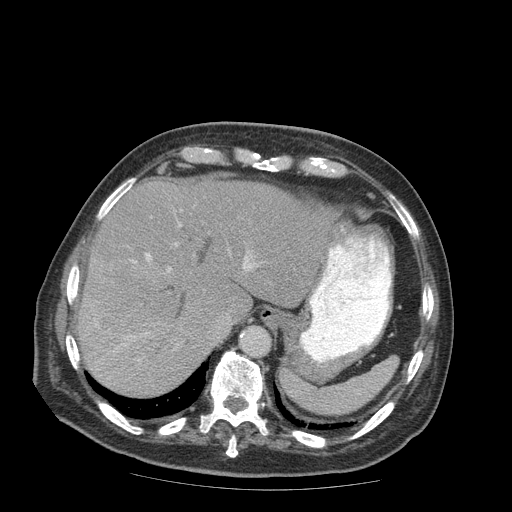
Contrast-enhanced abdominal CT (liver protocol), one axial slice. Slice 67 of 99 in the series (ordered by position). Reconstruction kernel STANDARD. 140 kVp. Soft-tissue window (W 400 / L 40 HU). 2.5 mm slice thickness. 512 × 512 image matrix, field of view 420 × 420 mm. Case-level facts recorded for this patient, not image findings: diagnosis: hepatocellular carcinoma (patient treated with transarterial chemoembolisation; whether this scan precedes or follows treatment is not stated here); TNM stage (as recorded): Stage-IIIB; Child-Pugh class: A; tumour nodularity: multinodular.
Structures marked on this image (semi-automatically segmented with operator editing):
- liver parenchyma outside the tumour (the mass and vessels are separate outlines, so this box may not span the whole liver): bounding box <78,178,348,396> (left, top, right, bottom; pixels)
- mass: <85,258,177,339>
- liver vessels: <95,222,257,352>